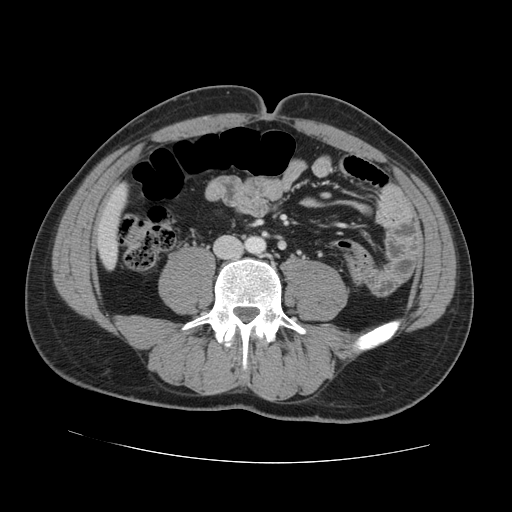
Contrast-enhanced abdominal CT, one axial slice. Slice 12 of 131 in the series (ordered by position). Intravenous contrast given. Soft-tissue window (W 400 / L 40 HU). 2.5 mm slice thickness. 512 × 512 image matrix. Male patient, age 40 years. Case-level facts recorded for this patient, not image findings: diagnosis: colorectal cancer liver metastases, imaged before liver resection; multiple liver metastases: yes; largest metastasis: 2.9 cm; disease in both lobes: yes.
Outlined on this slice (manually delineated by an expert):
- liver: box from (x=98, y=190) to (x=126, y=265) px